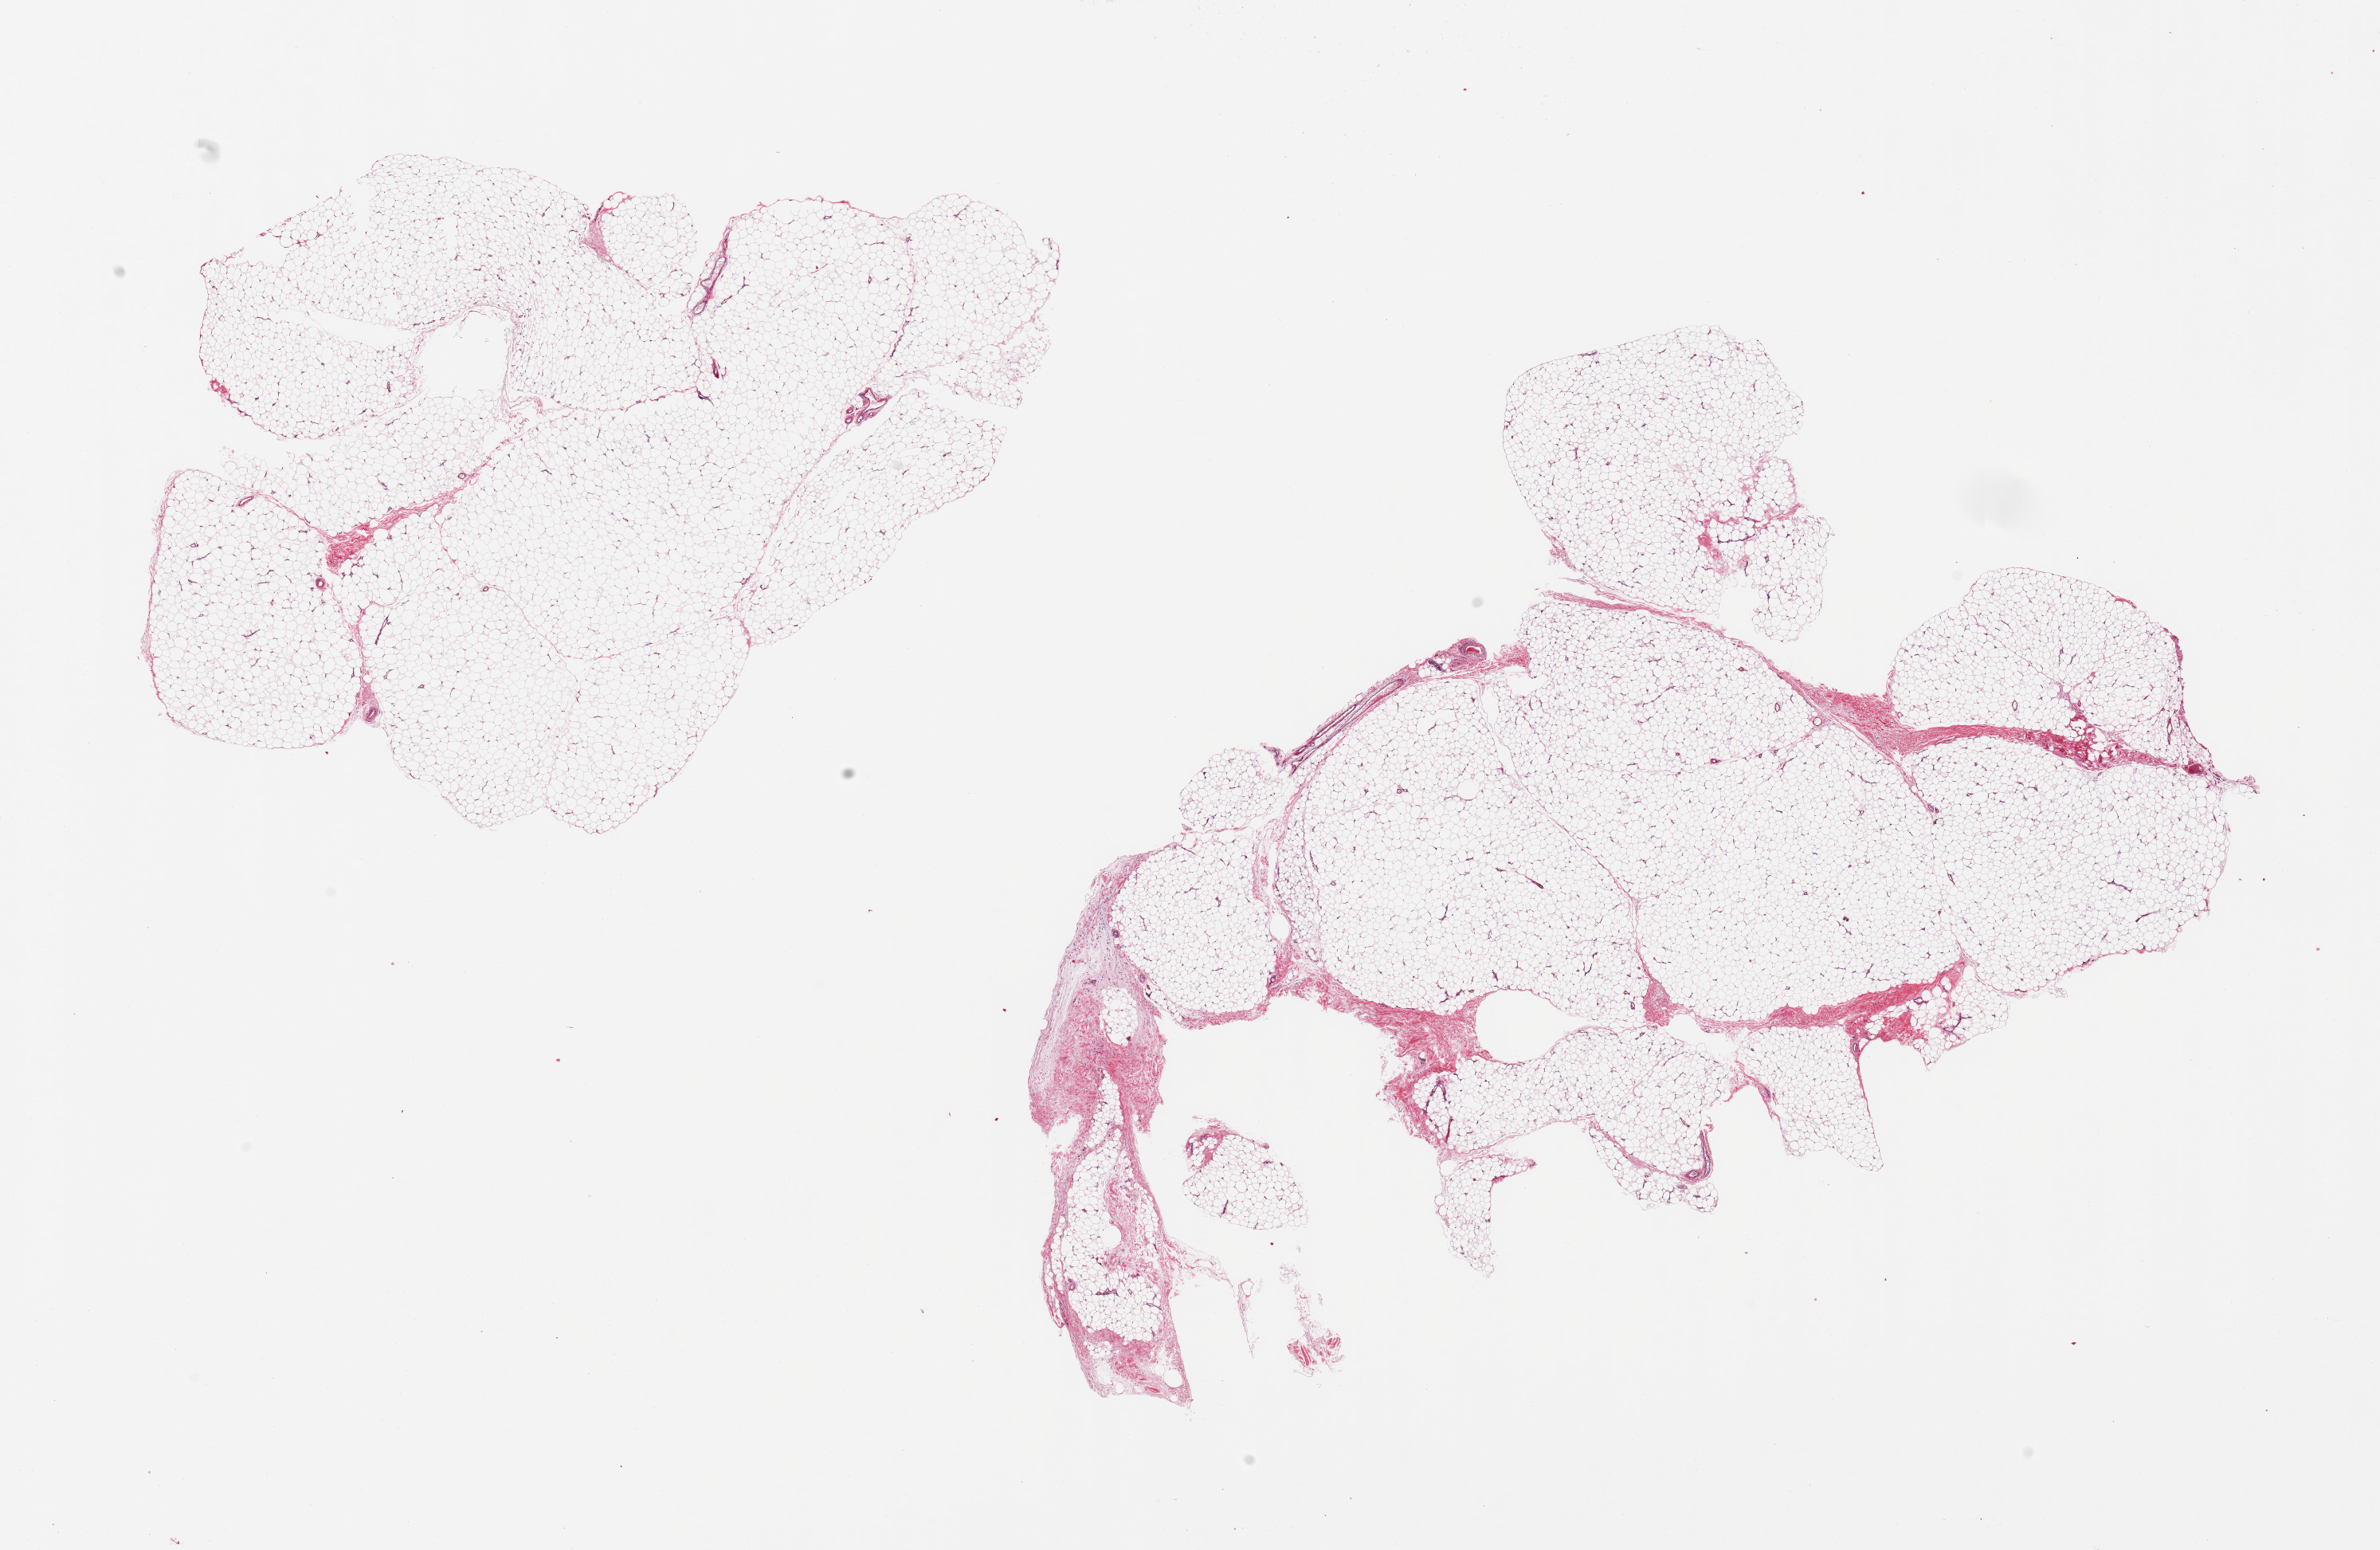
Whole-slide image, hematoxylin and eosin (H&E) stain, shown as a low-resolution overview of the whole scanned area (about 23.6 x 15.4 mm). PAXgene-fixed, paraffin-embedded tissue. Sampled site (target tissue): adipose tissue. Donor tissue sample. Donor sex: male.
- review note (as recorded): pieces, ~5-10% fascia/vascular elements